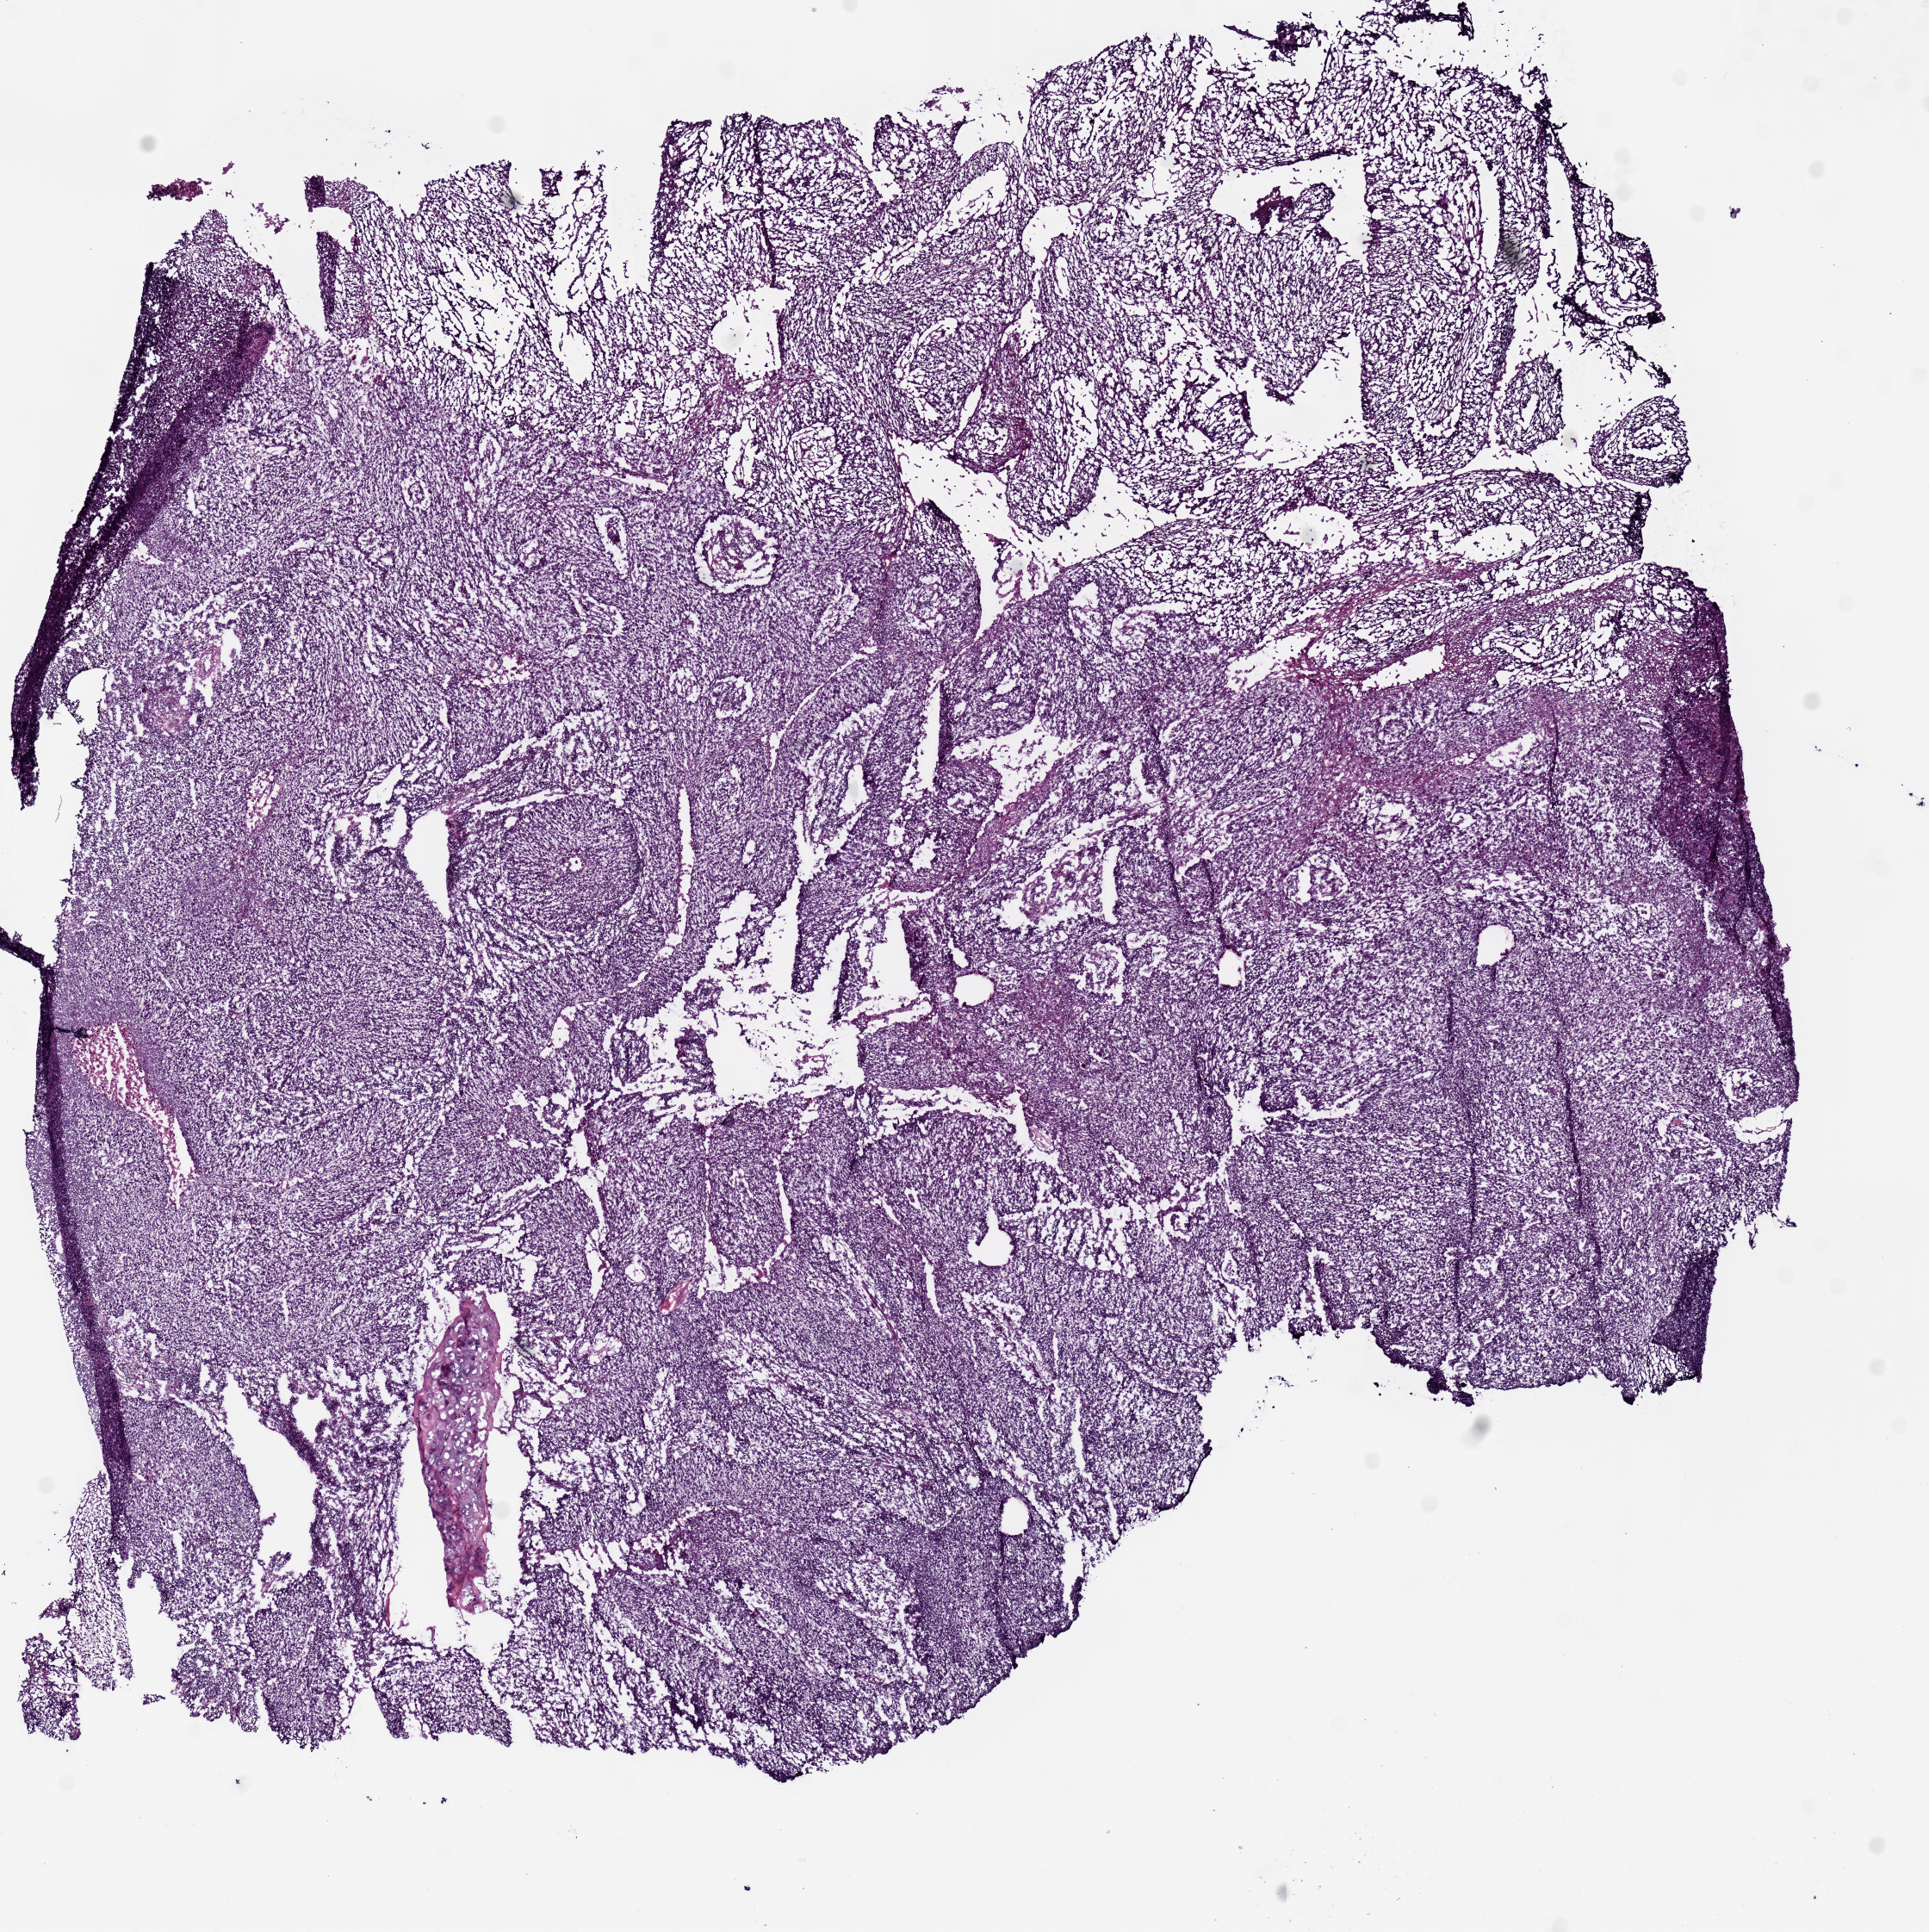
Whole-slide histology image, Hematoxylin and eosin (H&E) stained — shown as a low-resolution overview of the whole scanned area (about 8.9 x 8.9 mm), frozen section from the top of the tissue portion, lung, primary tumour sample. Male, age 58 years at initial diagnosis. Slide review estimates, as recorded: tumour nuclei 70%, necrosis 5%.
Laterality: right. Diagnosis: Squamous cell carcinoma, NOS (upper lobe, lung).